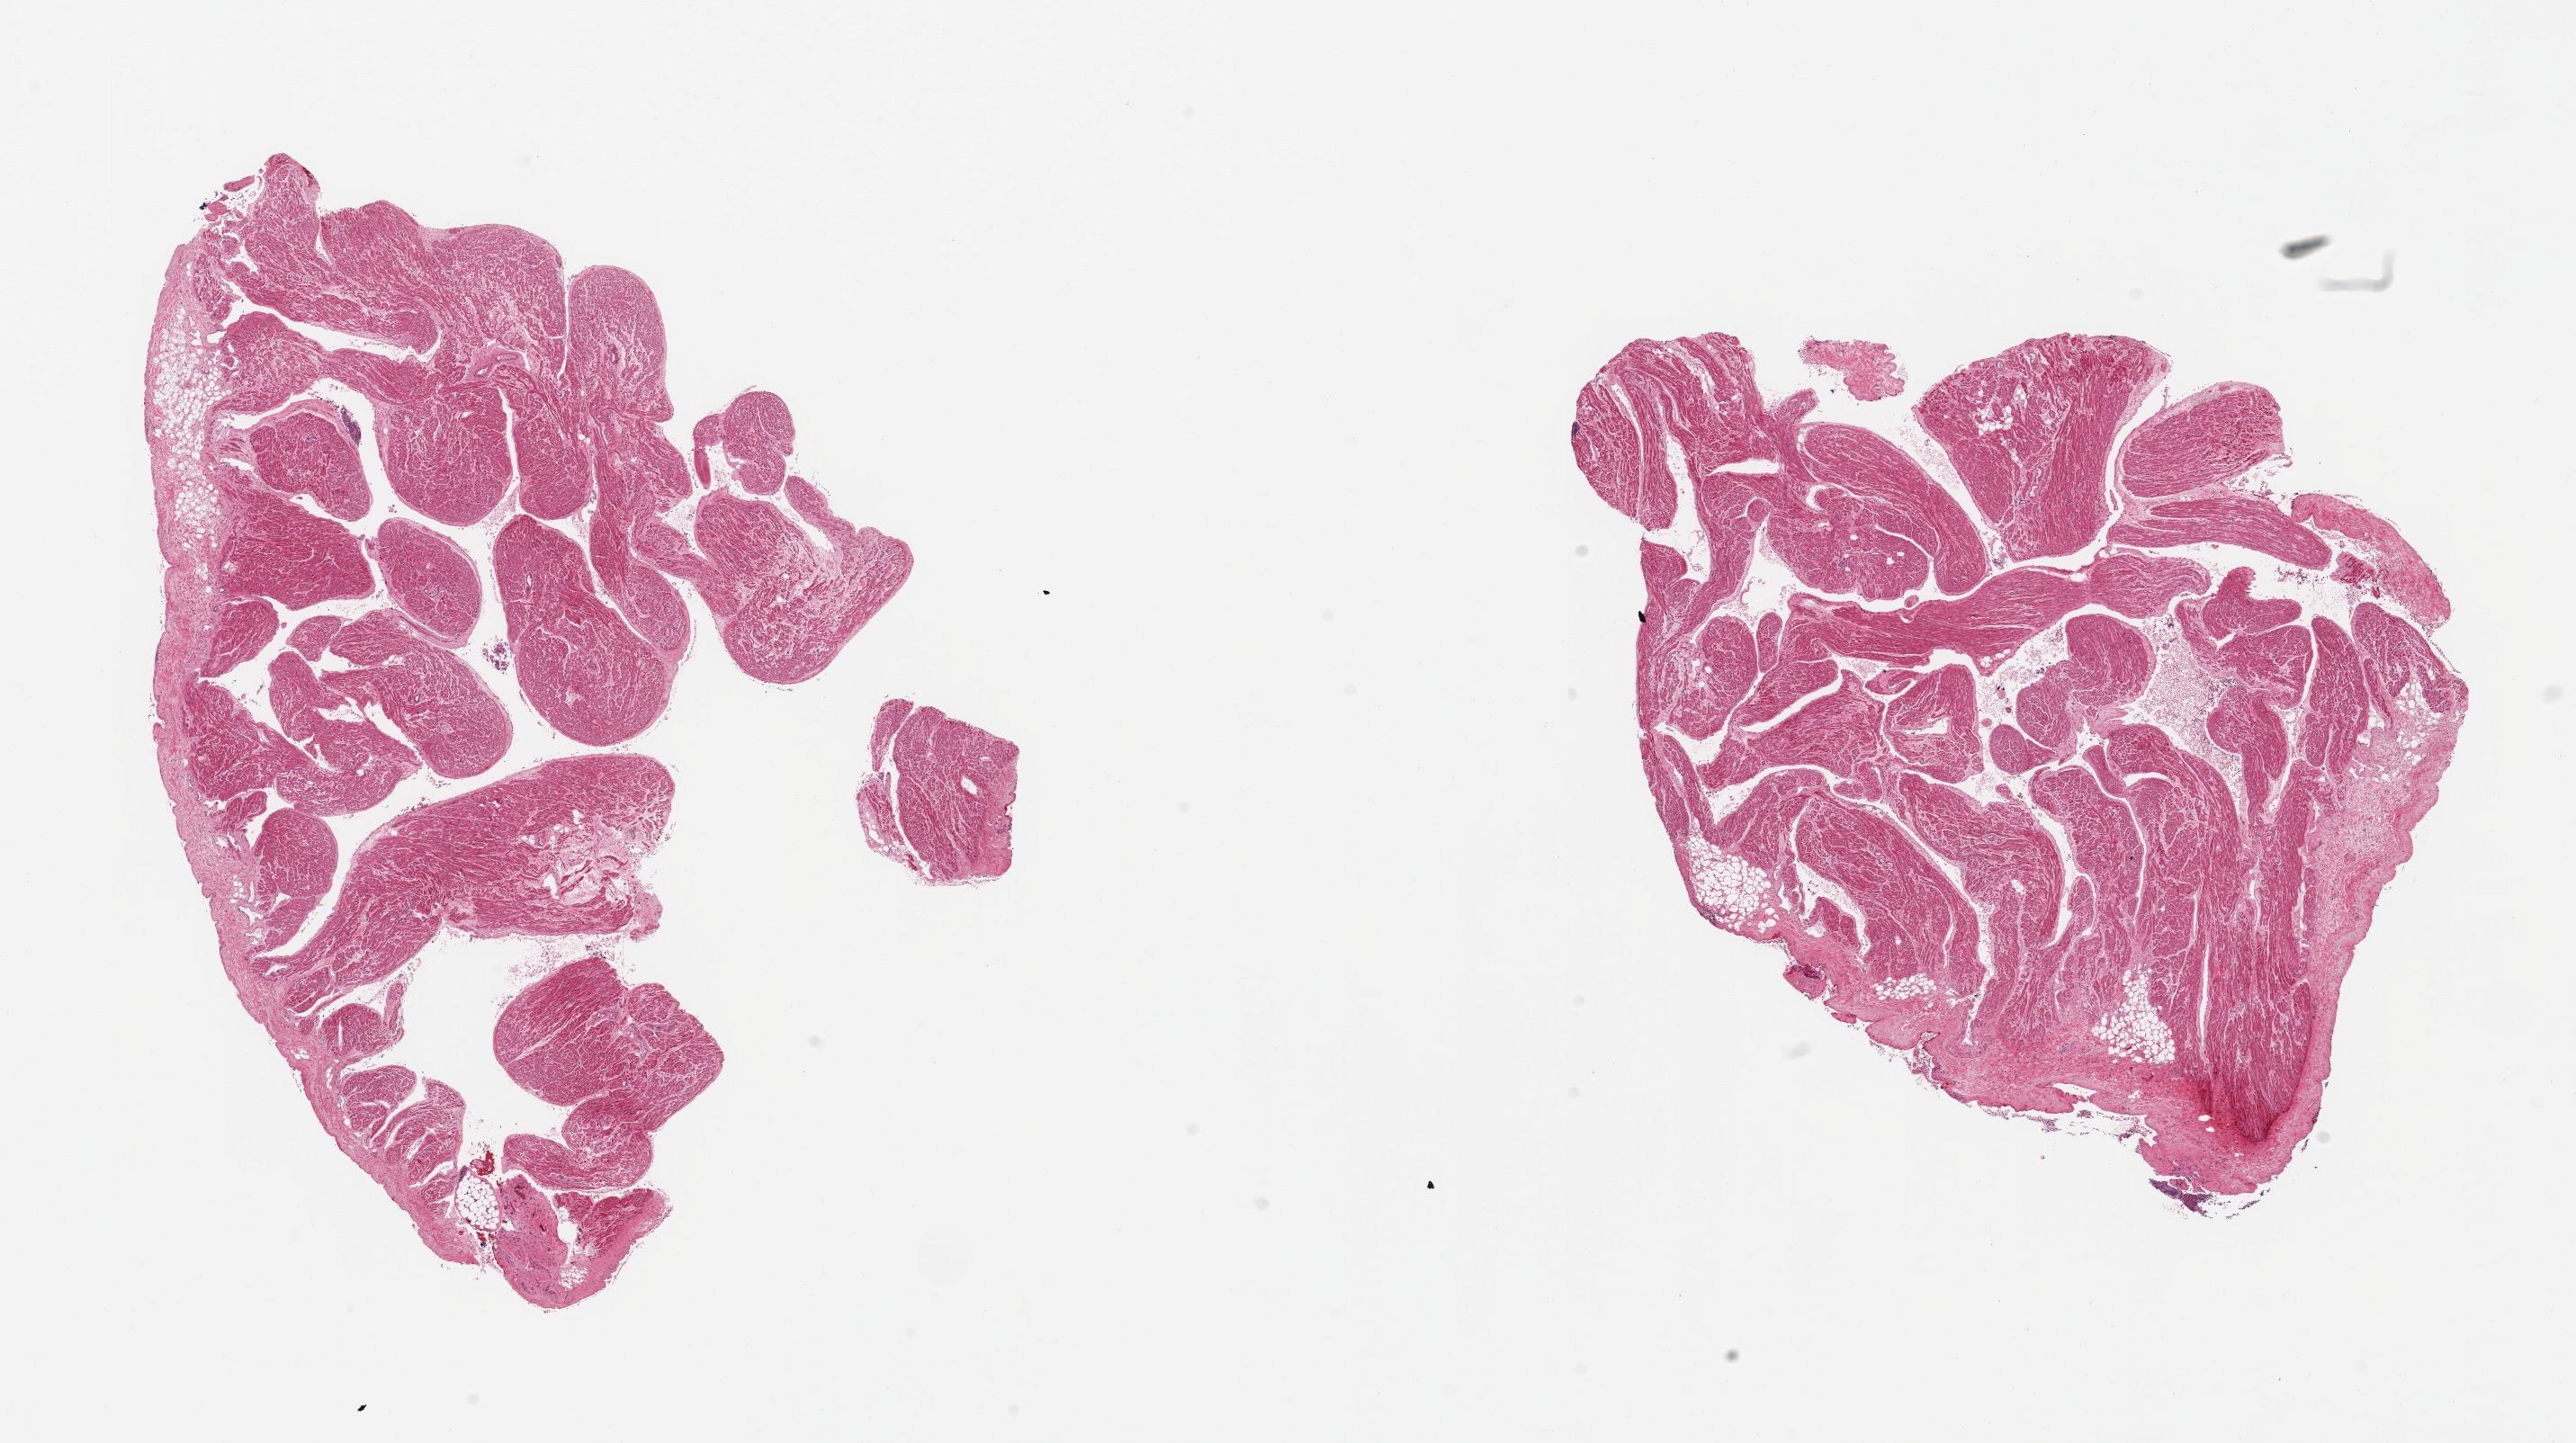
Digitized haematoxylin and eosin-stained section, brightfield — shown as a low-resolution overview of the whole scanned area (about 22.6 x 12.7 mm), PAXgene-fixed paraffin-embedded (PFPE) section, sampled site (target tissue): auricular appendage, tissue donor sample. Donor: male.
Review note (as recorded): 2 pieces, minimal abnormalities.